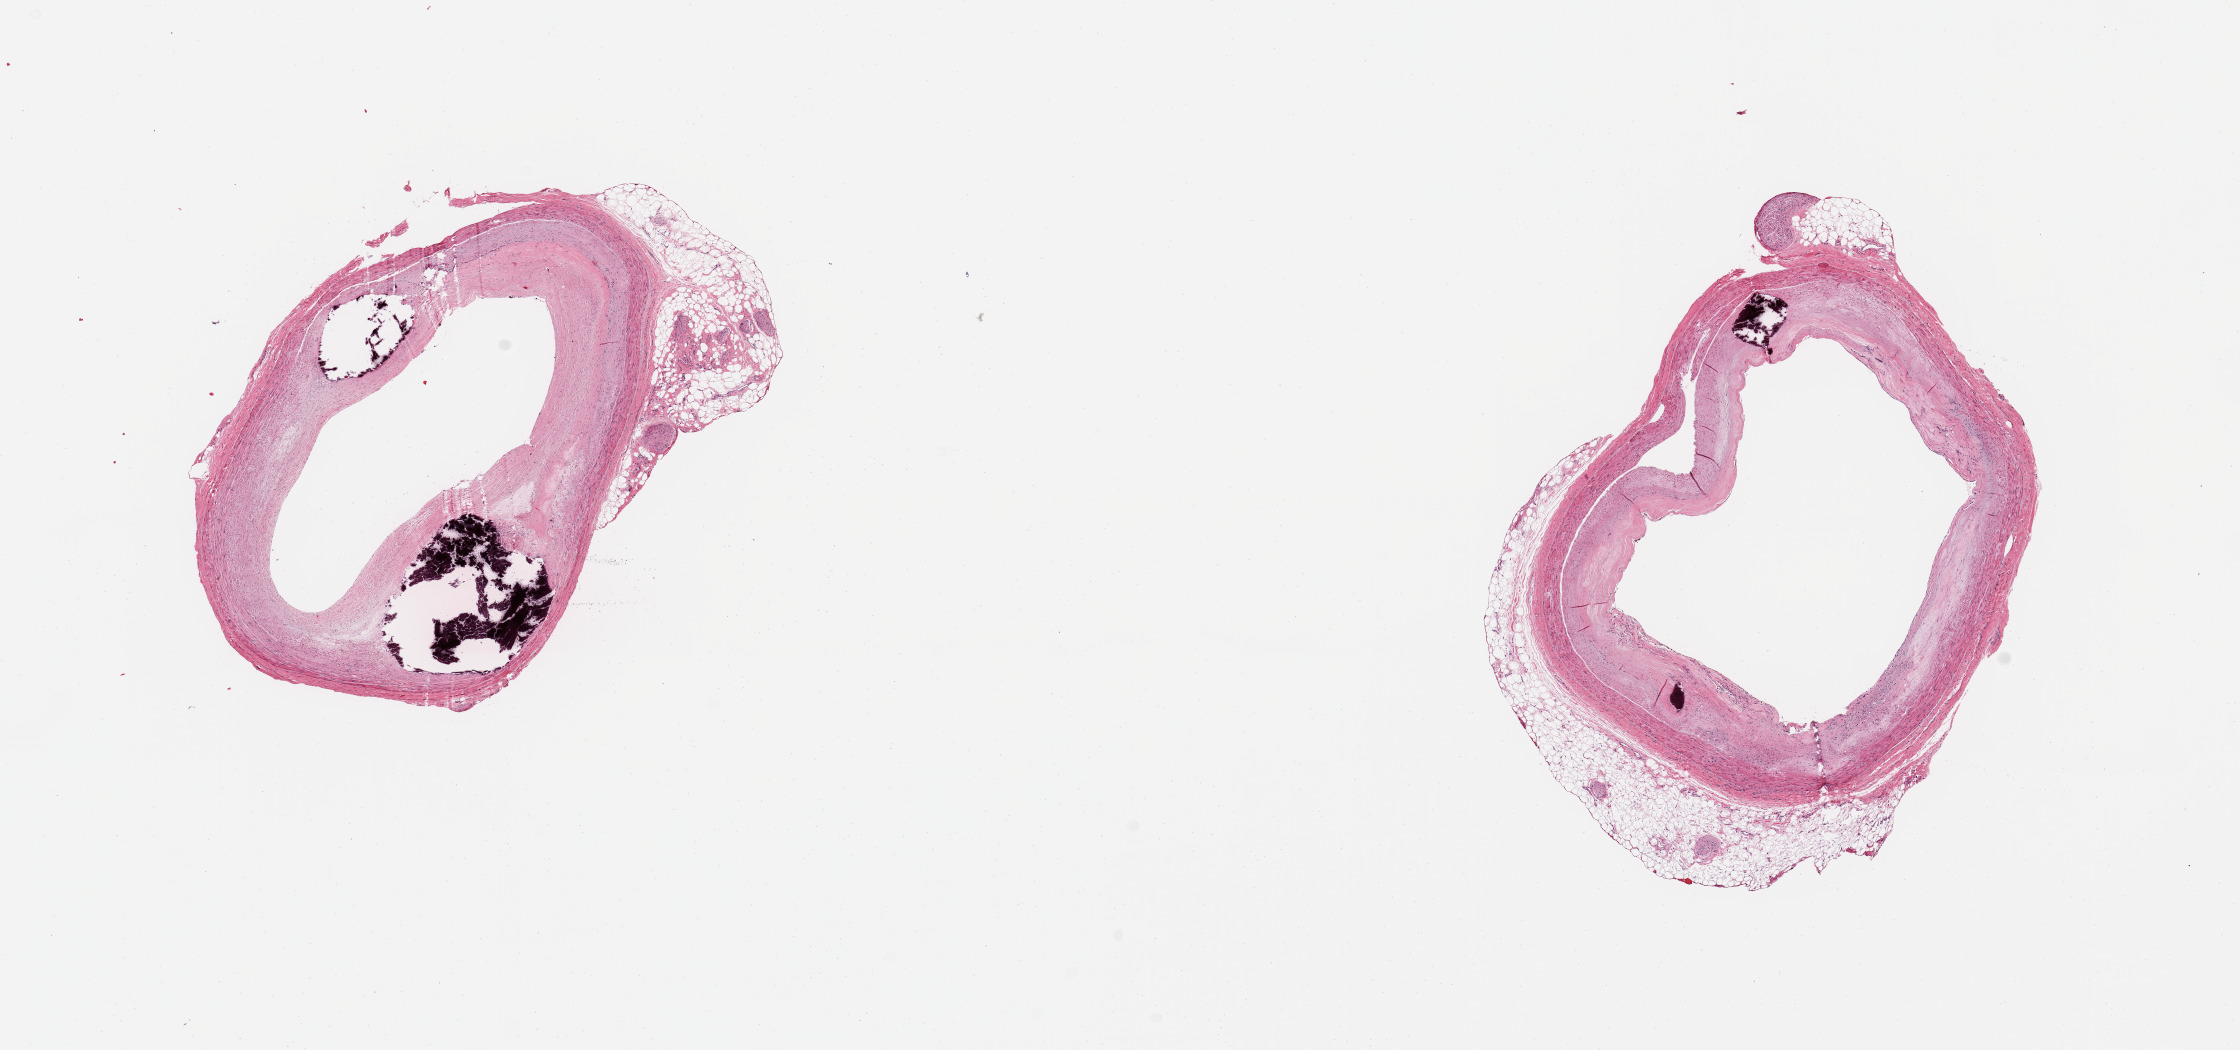
Whole-slide image, H&E stain, whole scanned area (about 17.7 x 8.3 mm) shown as a low-resolution overview, PAXgene-fixed paraffin-embedded (PFPE) section, target tissue: coronary artery, tissue donor sample. Donor: female.
- reviewer comment on this tissue sample: 2 pieces, calcifying atherosis, ~60% occlusive; partial rims adherent epicardial fat up to ~1mm